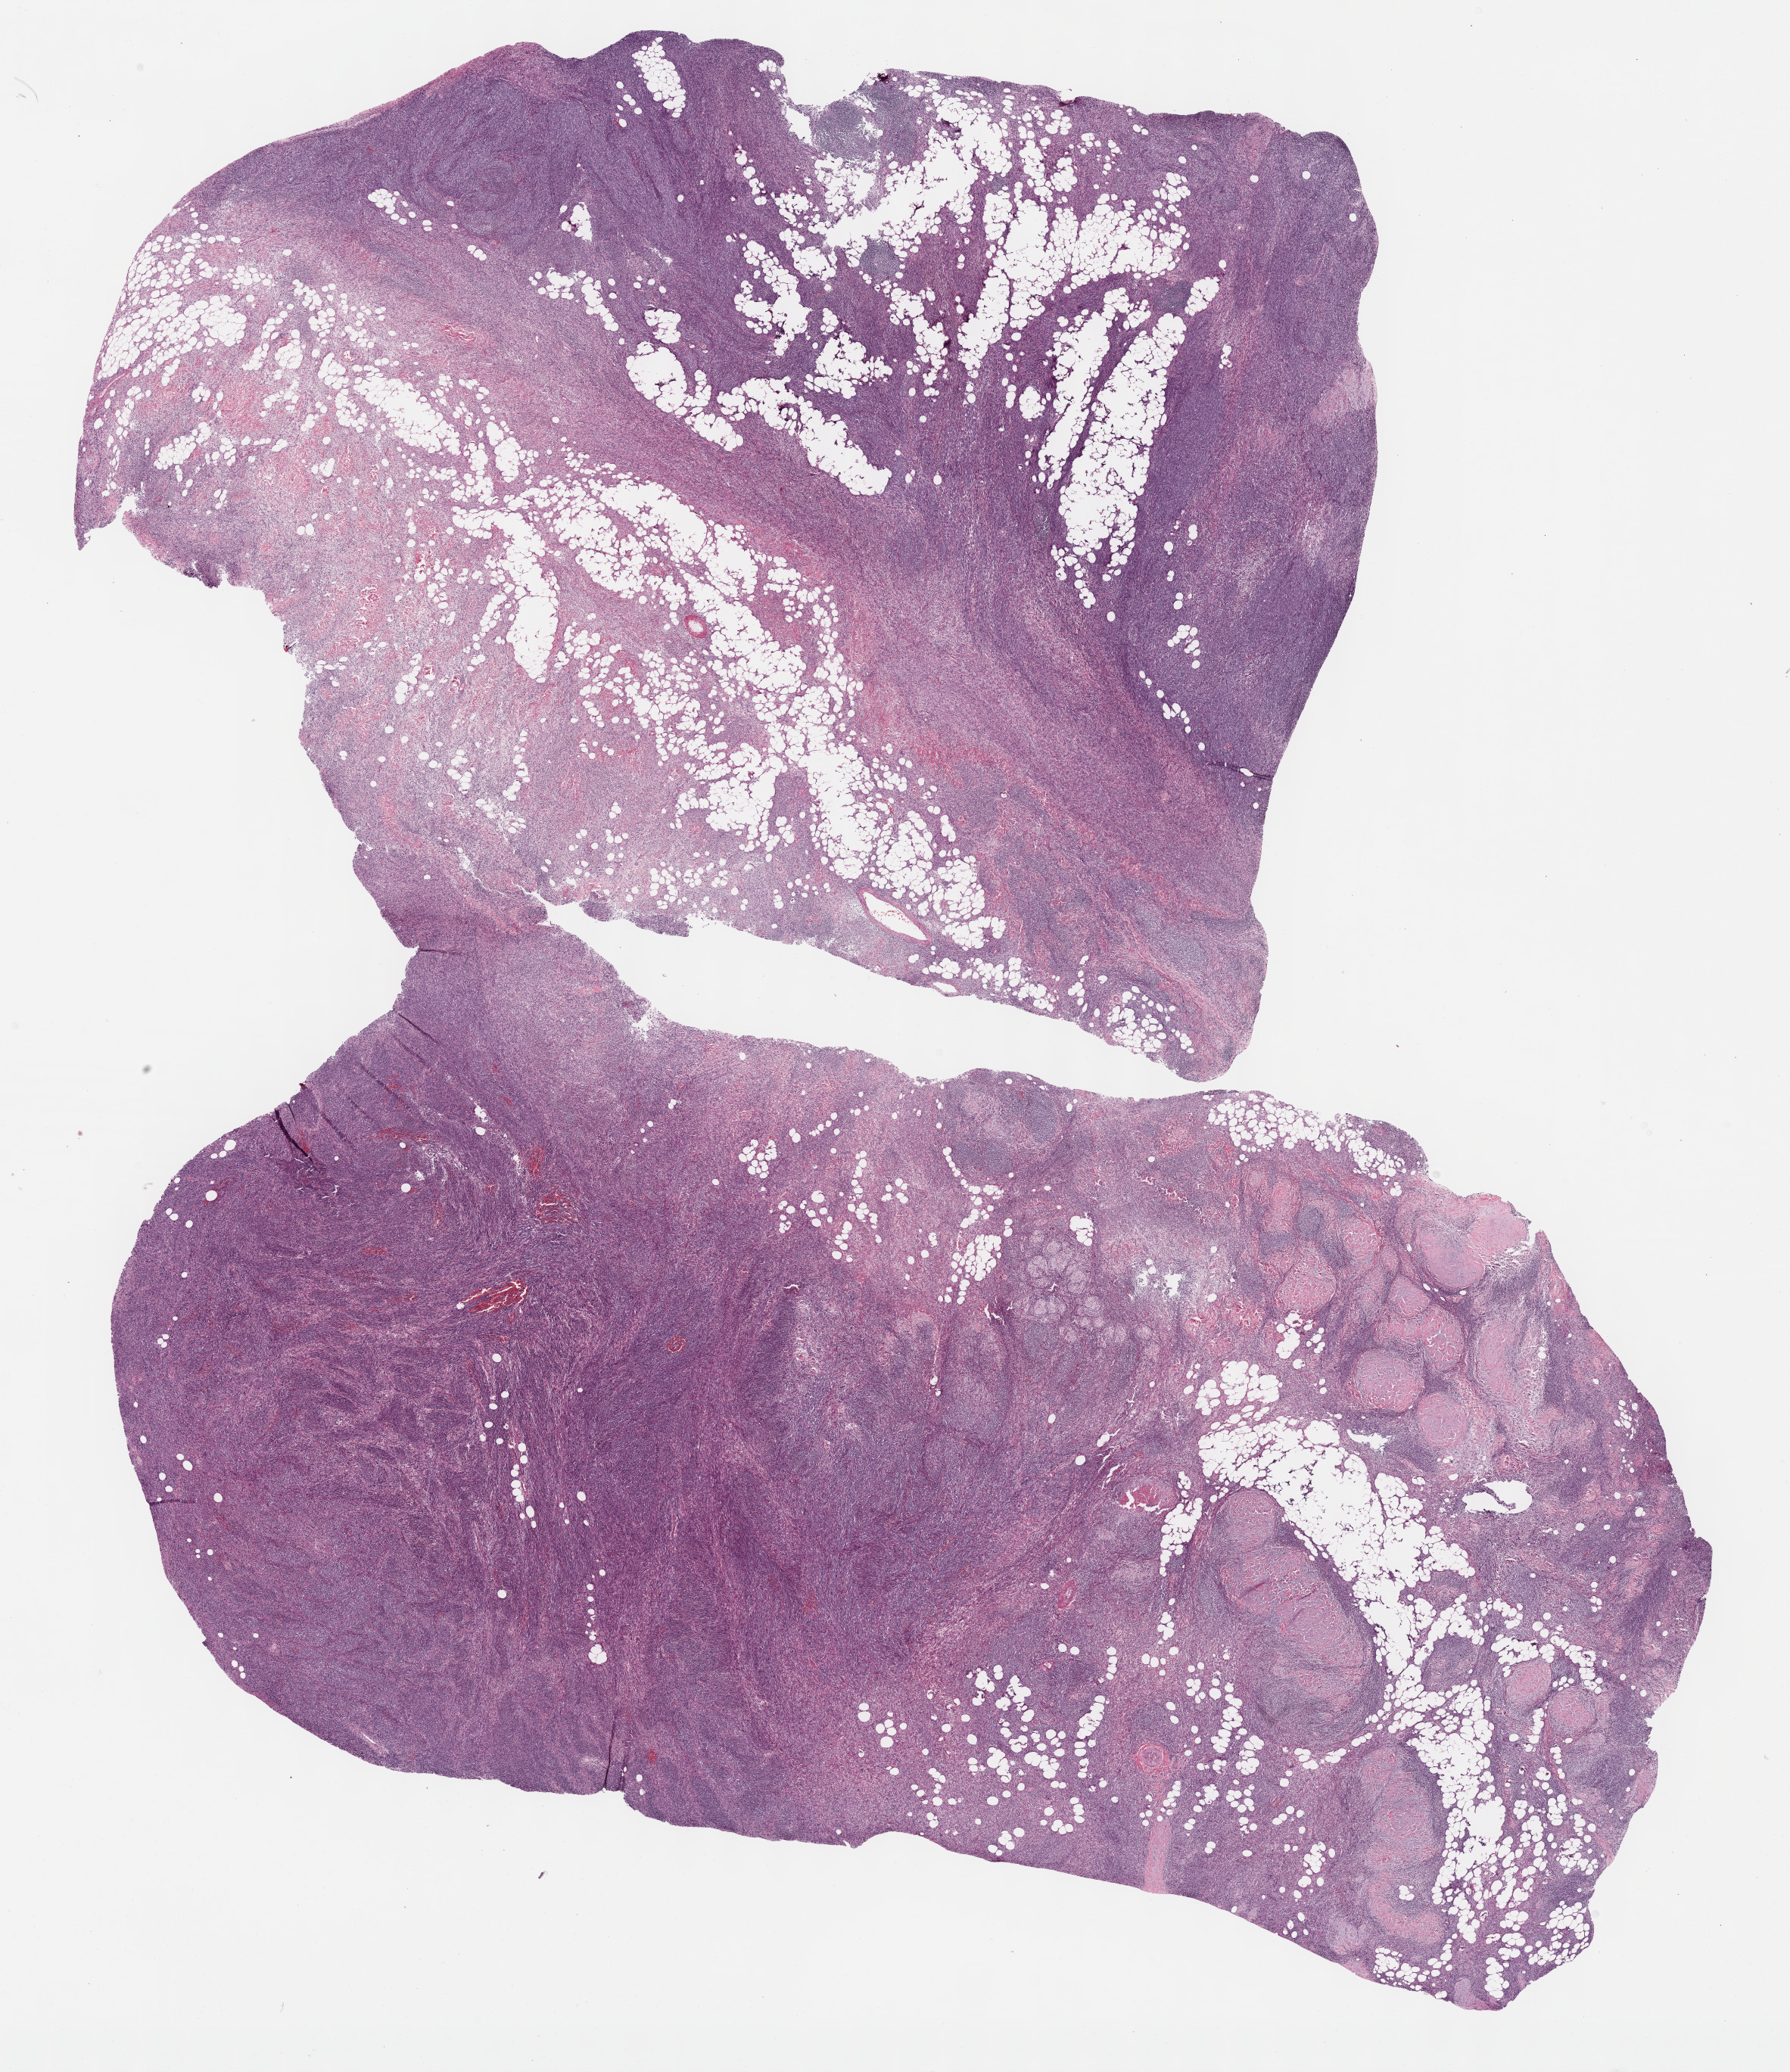
Whole-slide histology image, H&E-stained, low-resolution overview of the scanned area, about 19.1 x 22.1 mm, formalin-fixed paraffin-embedded (FFPE) diagnostic section, sample: primary tumour, connective, subcutaneous and other soft tissues. Patient: female, age at initial diagnosis 28 years.
Pathologic diagnosis: Synovial sarcoma, spindle cell (connective, subcutaneous and other soft tissues of lower limb and hip).